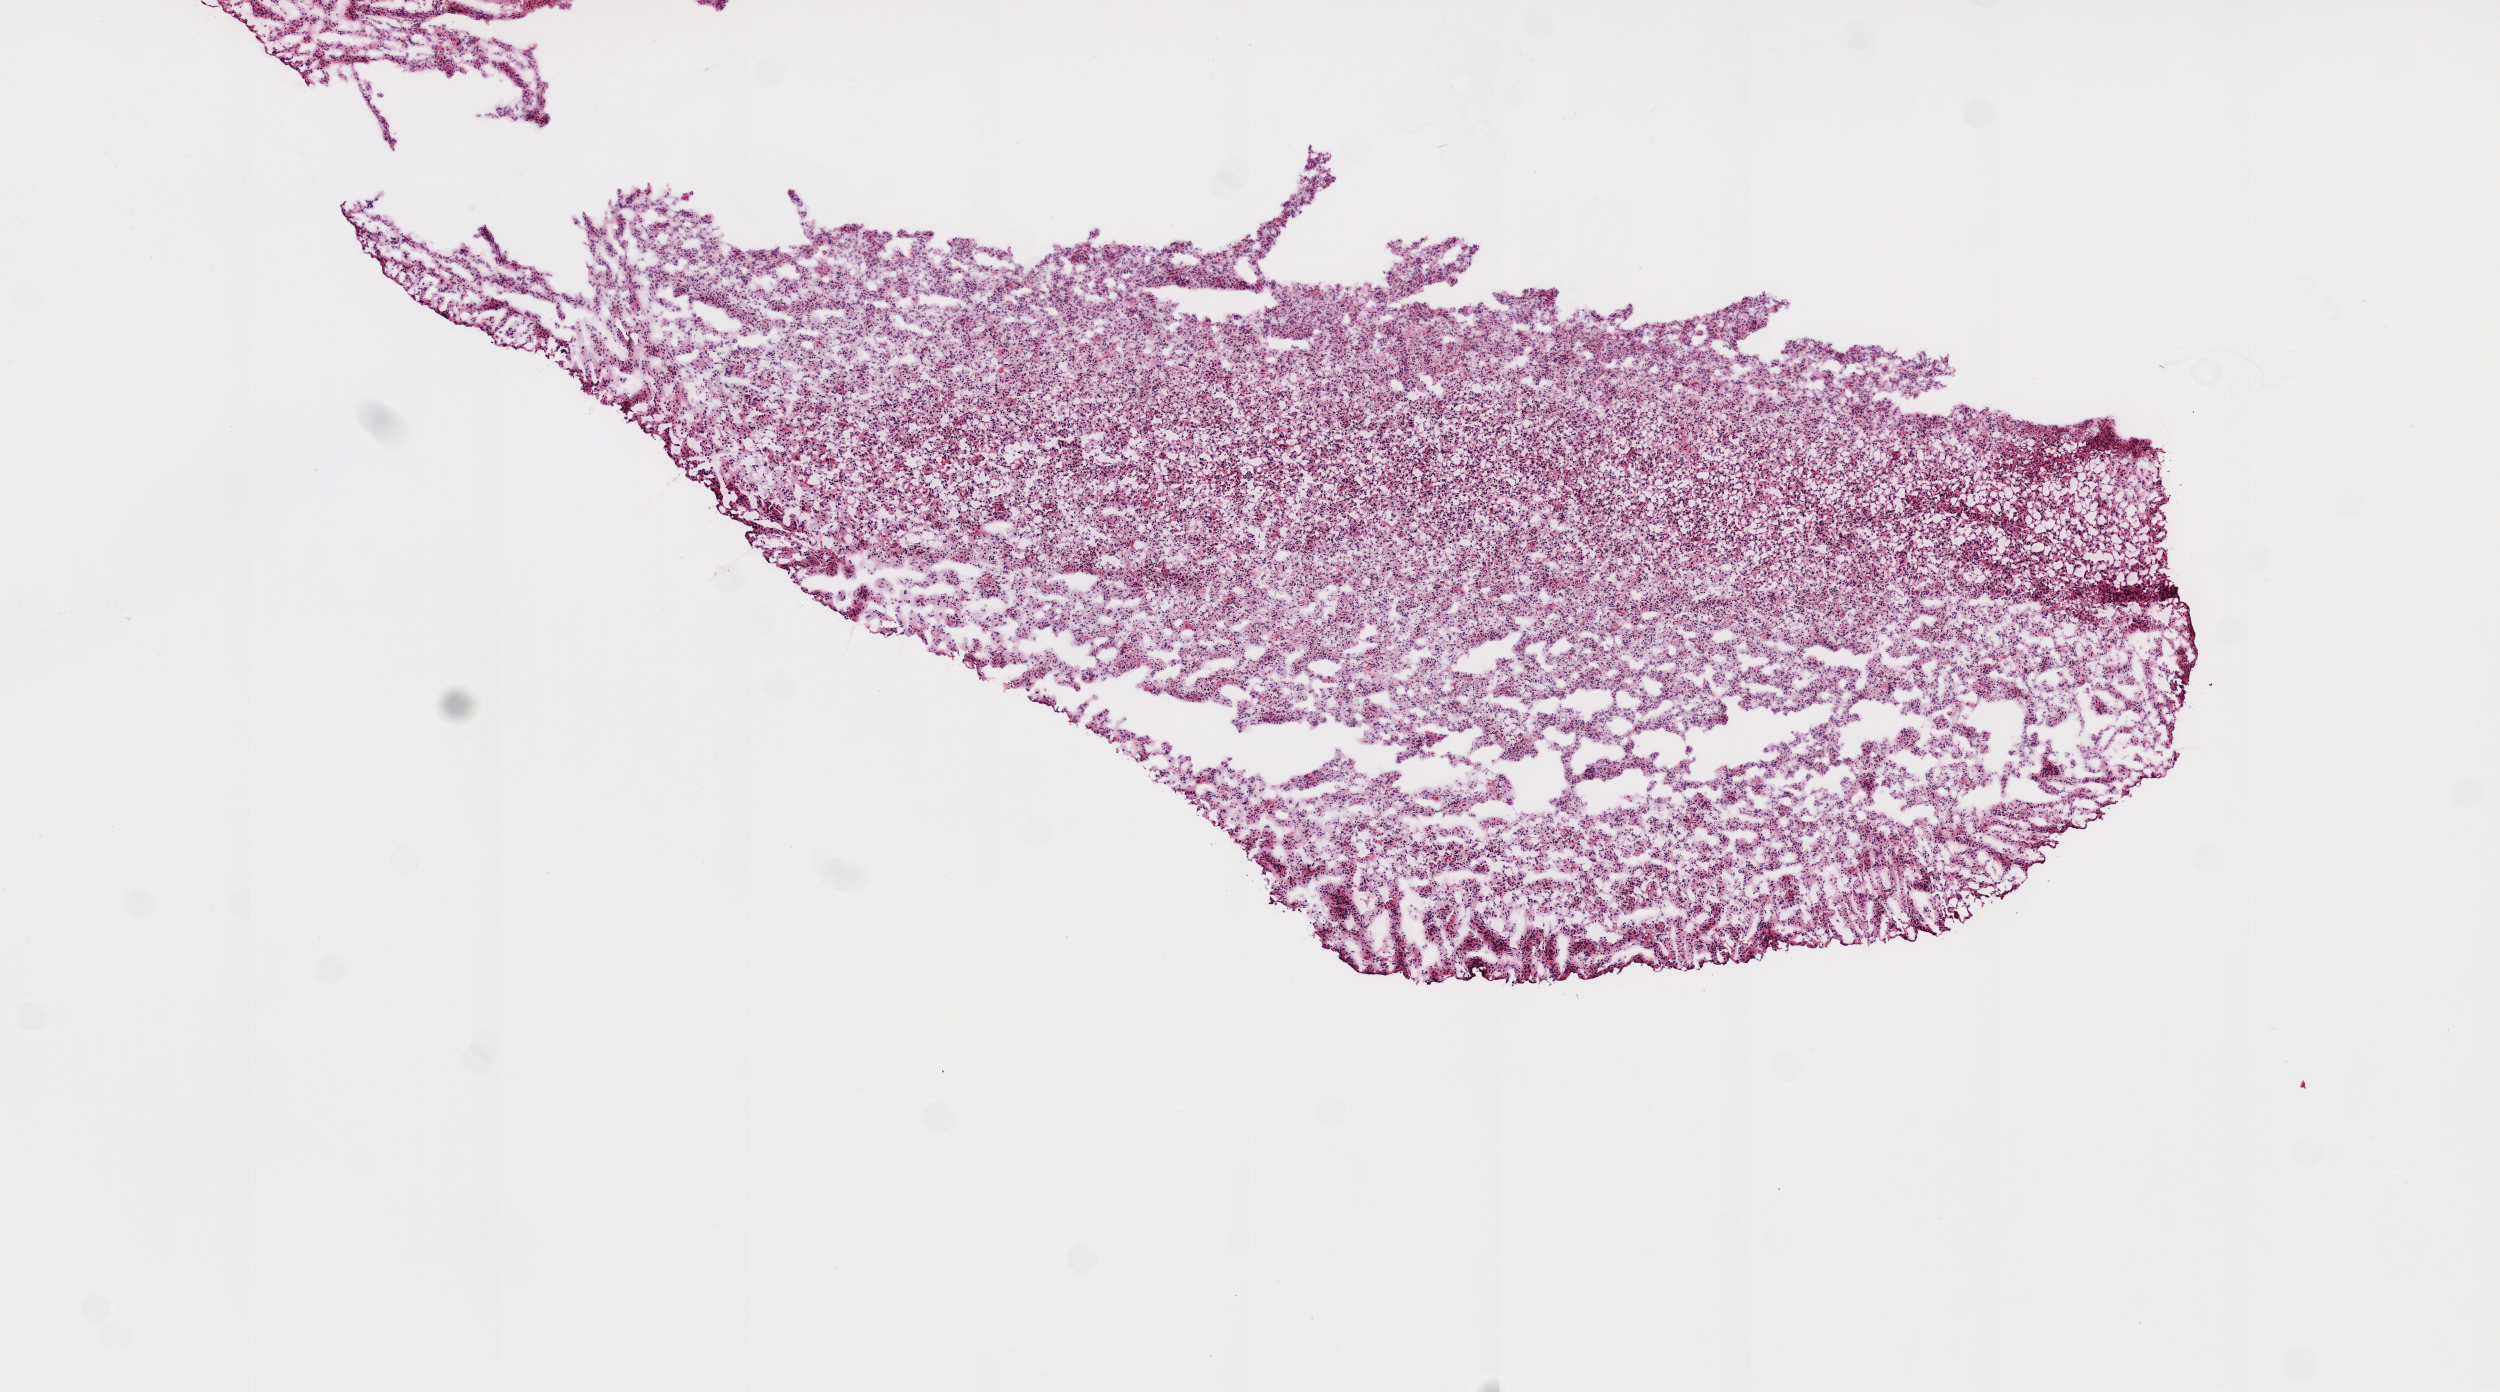
Digitized H&E-stained tissue section (whole slide) — low-resolution overview of the scanned area, about 10.0 x 5.6 mm (from a 20x scan), frozen section from the top of the tissue portion, primary tumour sample from the brain. Patient: male, age at initial diagnosis 42 years. Histologic grade: G3 (poorly differentiated). Pathologist review of this section (percent, as recorded): tumour cells 100%, tumour nuclei 80%, normal cells 0%, stromal cells 0%, necrosis 0%.
• histologic diagnosis: Astrocytoma, anaplastic
• laterality: right